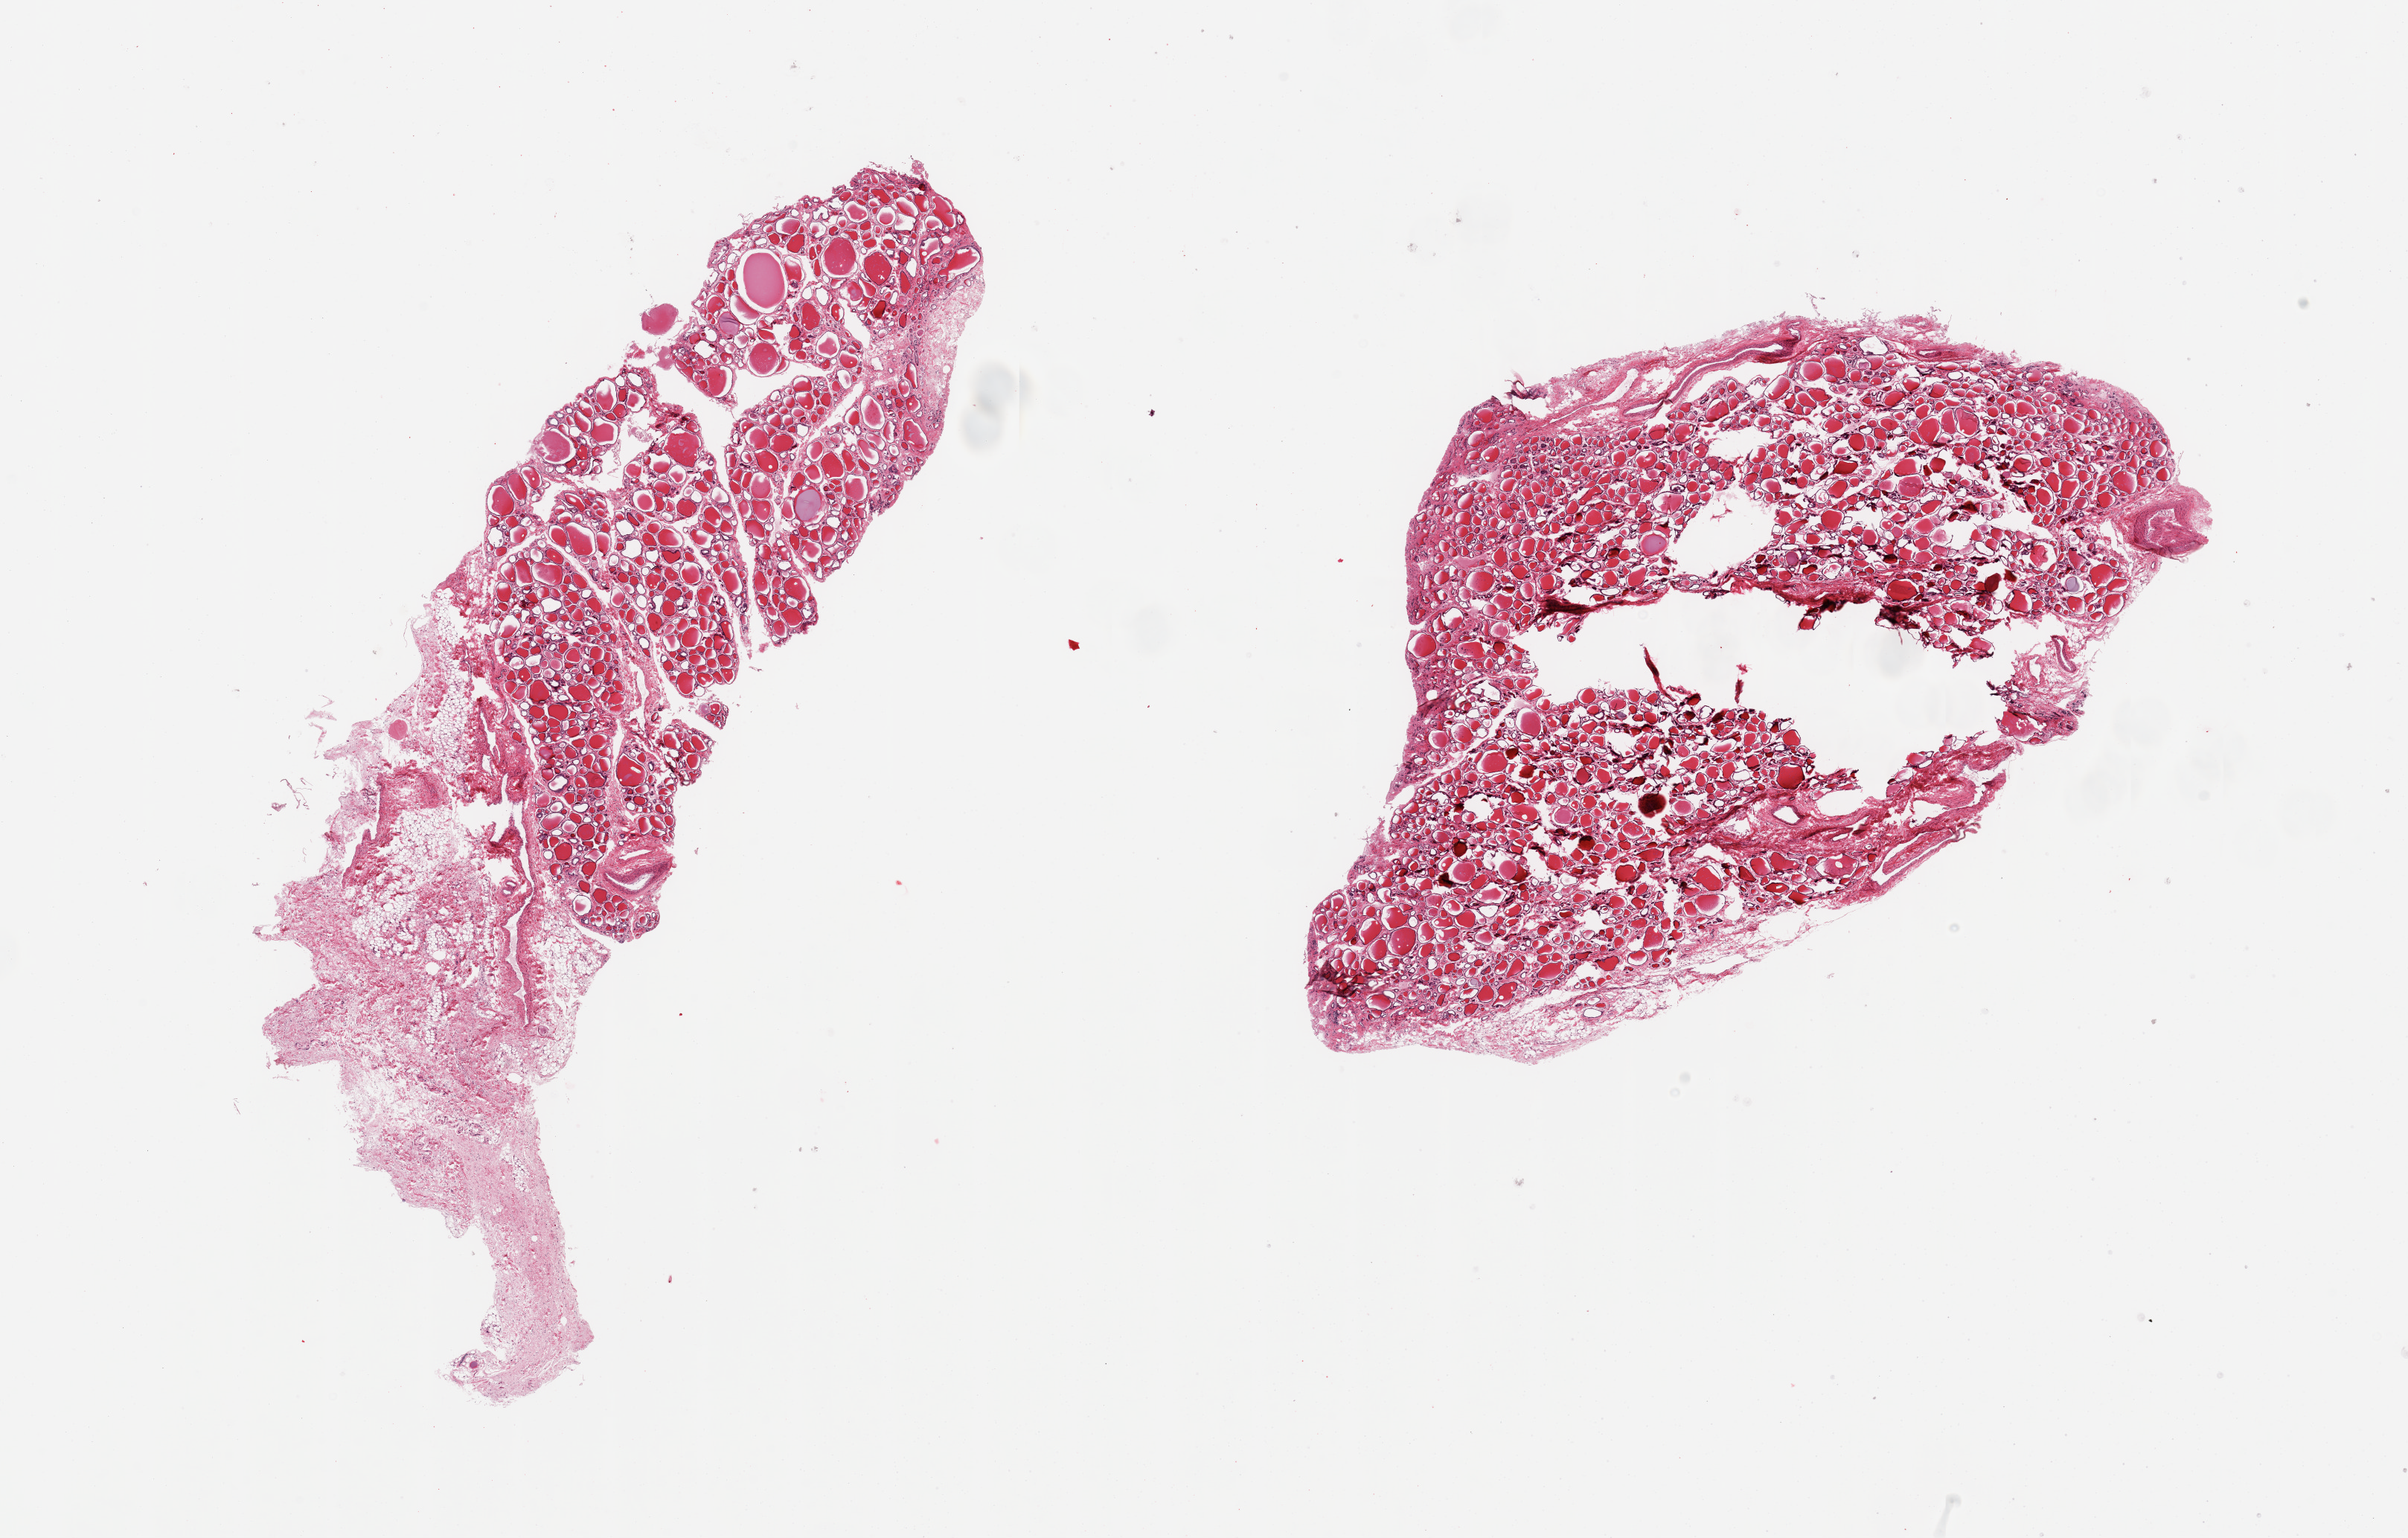
Digitized haematoxylin and eosin-stained section, brightfield, shown as a low-resolution overview of the whole scanned area (about 25.6 x 16.3 mm). PAXgene-fixed, paraffin-embedded tissue. Section of thyroid (target tissue). Donor tissue sample. Donor sex: male.
* review note (as recorded): 2 pieces; one with ~50% of fibrovascular and adipose tissue attached; other with central empty spaces (, ? poor fixation)